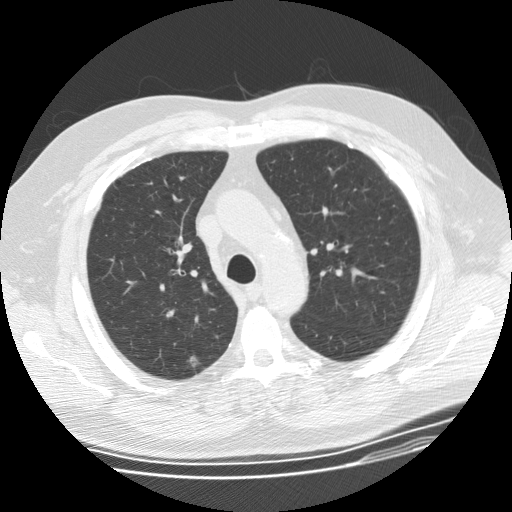
Low-dose screening chest CT, one axial slice; slice 109 of 155 in the series (ordered by position); 120 kVp; lung window (W 1500 / L -600 HU); 2.5 mm slice thickness; 512 × 512 image matrix, field of view 380 × 380 mm.
Structures marked on this image (outlined manually by an expert reader):
- lesion 1 (tumor, upper lobe of right lung): box from (x=187, y=355) to (x=201, y=367) px